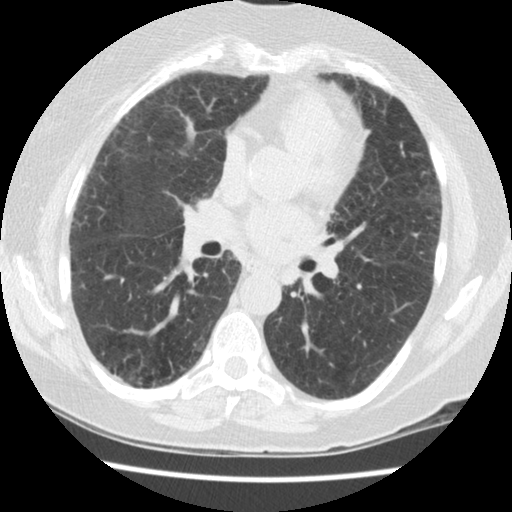
Chest CT (low-dose screening protocol), one axial image. Second screening round (one year after baseline). Lung window (W 1500 / L -600 HU). Standard (soft-tissue) reconstruction kernel (STANDARD). Slice 65 of 134 in the series. 512 × 512 image matrix. Female participant, aged 60 years at enrolment. Former smoker at enrolment.
Lesion marked by an expert reader, bounding box <270,255,316,300> (left, top, right, bottom; pixels). Screening reader's record for this exam (one nodule recorded; not confirmed to be the boxed lesion): non-calcified nodule or mass ≥4 mm, left lower lobe, 5 × 4 mm, smooth margins, soft tissue attenuation, pre-existing on the prior screen: yes; interval growth: no. Official screen result: positive, no significant change: stable abnormalities potentially related to lung cancer, unchanged since the prior screening exam. Later outcome: lung cancer diagnosed 423 days after this screen — small cell carcinoma, NOS, left lower lobe, undifferentiated (G4), stage IV (AJCC 6th edition), 69 mm at pathology.